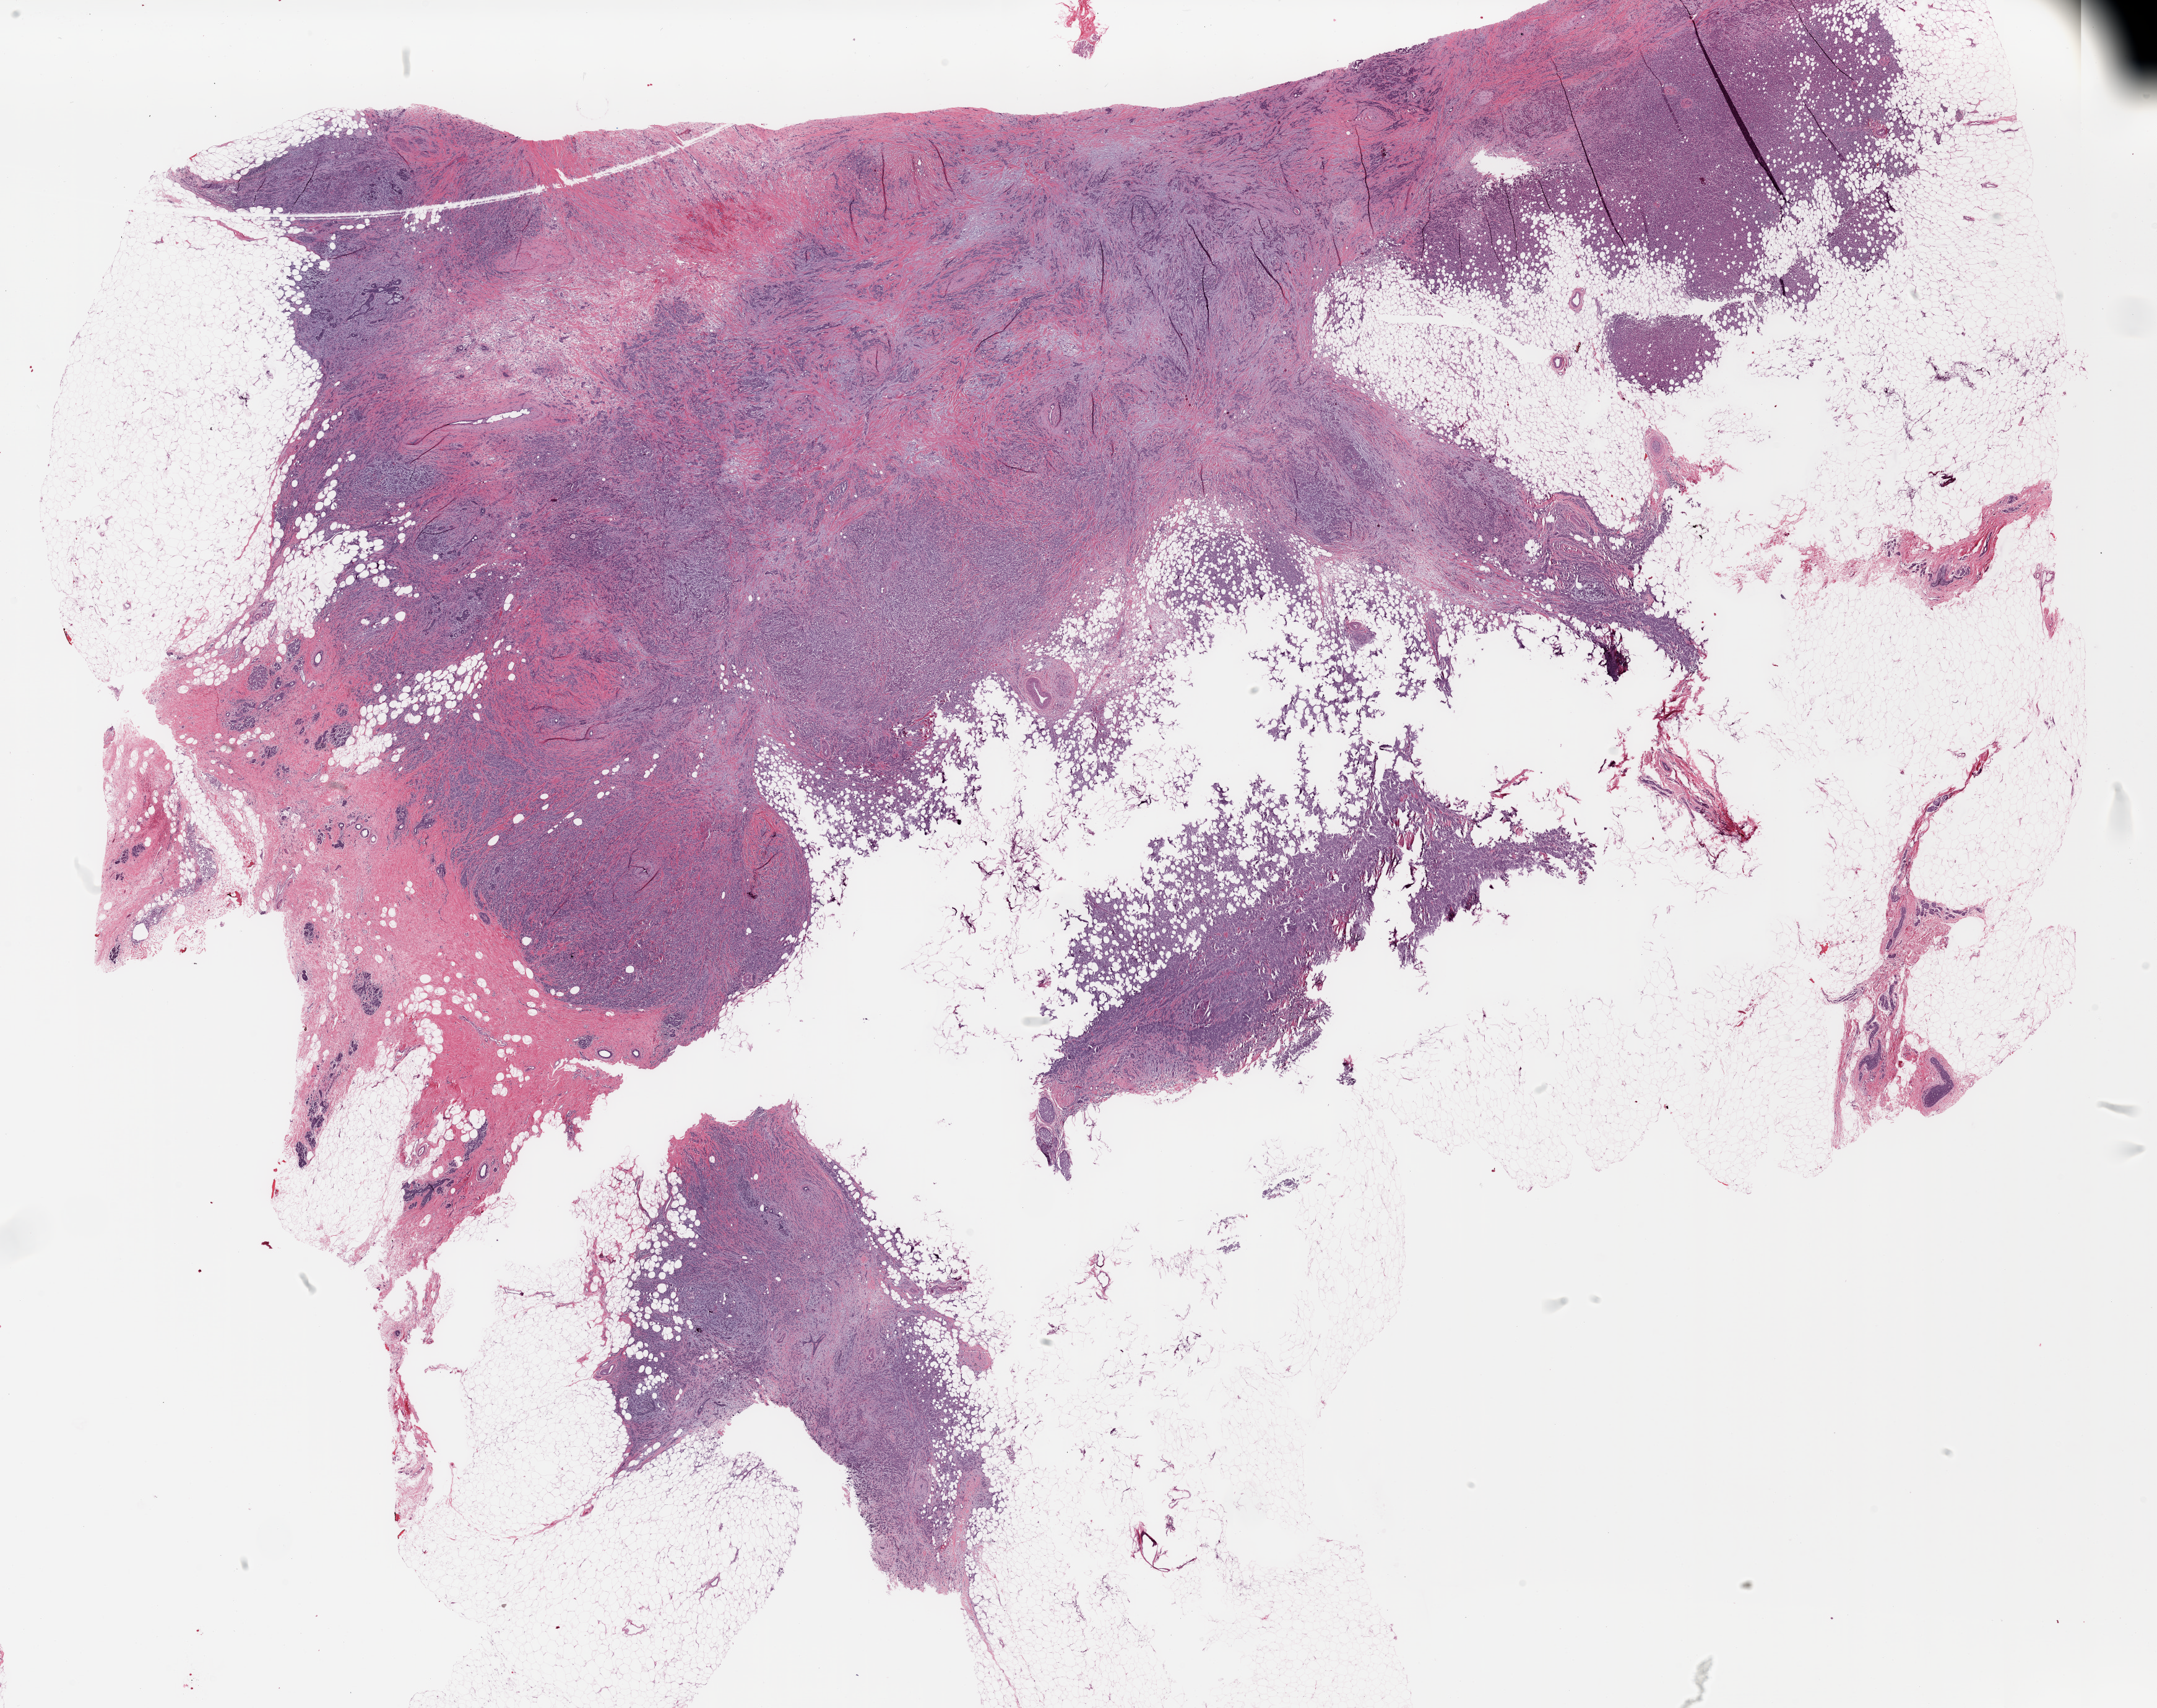
Whole-slide histology image, Hematoxylin and eosin (H&E) stained, shown as a low-resolution overview of the whole scanned area (about 27.8 x 22.1 mm, from a 20x scan), formalin-fixed paraffin-embedded (FFPE) diagnostic section, breast, primary tumour sample. Patient: female, age at initial diagnosis 61 years.
- pathologic diagnosis: Lobular carcinoma, NOS
- AJCC pathologic stage: IIIC